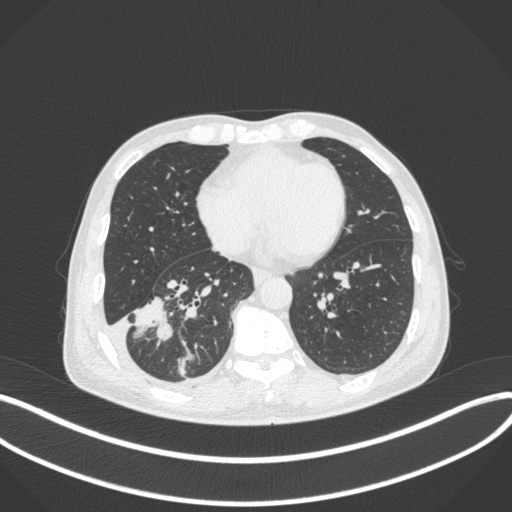
Chest CT, one axial slice. Slice 141 of 385 in the series (ordered by position). 120 kVp. Lung window (W 1500 / L -600 HU). 1 mm slice thickness. 512 × 512 image matrix, field of view 400 × 400 mm. Patient: male, 64 years. Case-level facts recorded for this patient, not image findings: clinical TNM (as recorded): T3 N0 M0; histopathological grade: G2-3.
Structures marked on this image (bounding box drawn by a radiologist):
- lung tumour (recorded histology: adenocarcinoma): bounding box (x1, y1, x2, y2) in pixels: (133, 291, 178, 349)